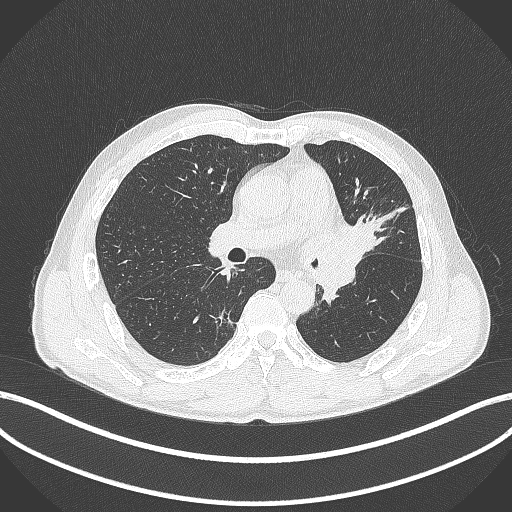
Chest CT, one axial slice; position 236 of 429 along the scan axis; lung window (W 1500 / L -600 HU); 1 mm slice thickness; 512 × 512 image matrix. Male patient, age 57 years. From the clinical record (not read from this slice): clinical TNM (as recorded): T2b N0 M0.
Structures marked on this image (rectangle marked by the reading radiologist):
- lung tumour (recorded histology: squamous cell carcinoma): bounding box [x1, y1, x2, y2] px = [342, 220, 379, 269]